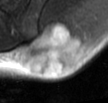
MRI of an extremity soft-tissue mass, one axial slice. Position 22 of 42 along the scan axis. T2-weighted fat-saturated. MR volume resampled by the dataset authors to the PET/CT grid (not the native acquisition matrix). 3.27 mm slice thickness. 108 × 103 image matrix, field of view 105 × 101 mm. Male patient. From the clinical record (not read from this slice): histological type: leiomyosarcoma; grade: intermediate; site of the primary tumour: left pelvis.
Annotated regions visible in this slice (expert contour drawn on MRI and transferred to this co-registered scan by the dataset authors):
- gross tumour volume (mass): bounding box [x1, y1, x2, y2] px = [19, 21, 88, 77]